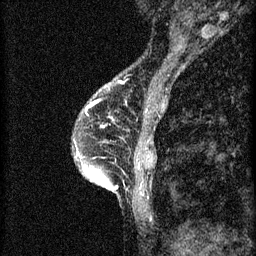
Breast MRI (dynamic contrast-enhanced), one sagittal slice. Slice 18 of 60 in the series (ordered by position). 3 images stored at this slice position (order not interpretable as contrast timing). 1.5 T. TE 4.2 ms, TR 8.2 ms. 2 mm slice thickness. 256 × 256 image matrix, field of view 180 × 180 mm. Patient: female, 45 years.
Annotated regions visible in this slice (semi-automatic segmentation, software-assisted and operator-edited):
- analysis volume of interest (the breast-tissue region the enhancement analysis was run in; not a lesion): bounding box <74,104,155,217> (left, top, right, bottom; pixels)
- tumour enhancement mask (voxels above the 70 % enhancement threshold inside the analysis volume of interest): <86,106,89,111>